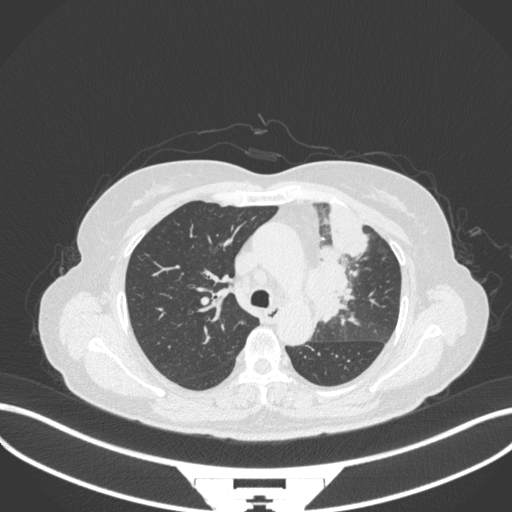
Chest CT, one axial slice; 120 kVp; lung window (W 1500 / L -600 HU); 1 mm slice thickness; 512 × 512 image matrix. Female patient, age 64 years. From the clinical record (not read from this slice): clinical TNM (as recorded): T2a N2 M0.
Structures marked on this image (bounding box drawn by a radiologist):
- lung tumour (recorded histology: adenocarcinoma): bounding box [x1, y1, x2, y2] px = [309, 200, 370, 328]